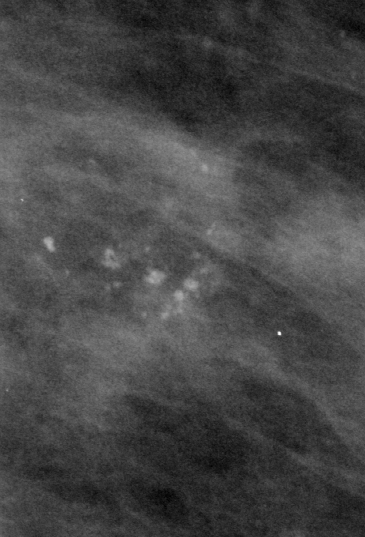
Crop from a digitized film mammogram around one marked abnormality, left breast, MLO view, BI-RADS breast density category 2 (scale 1–4).
Finding: calcifications, morphology amorphous, distribution clustered; BI-RADS assessment category 4; pathology result (as recorded, not read from the image): benign.